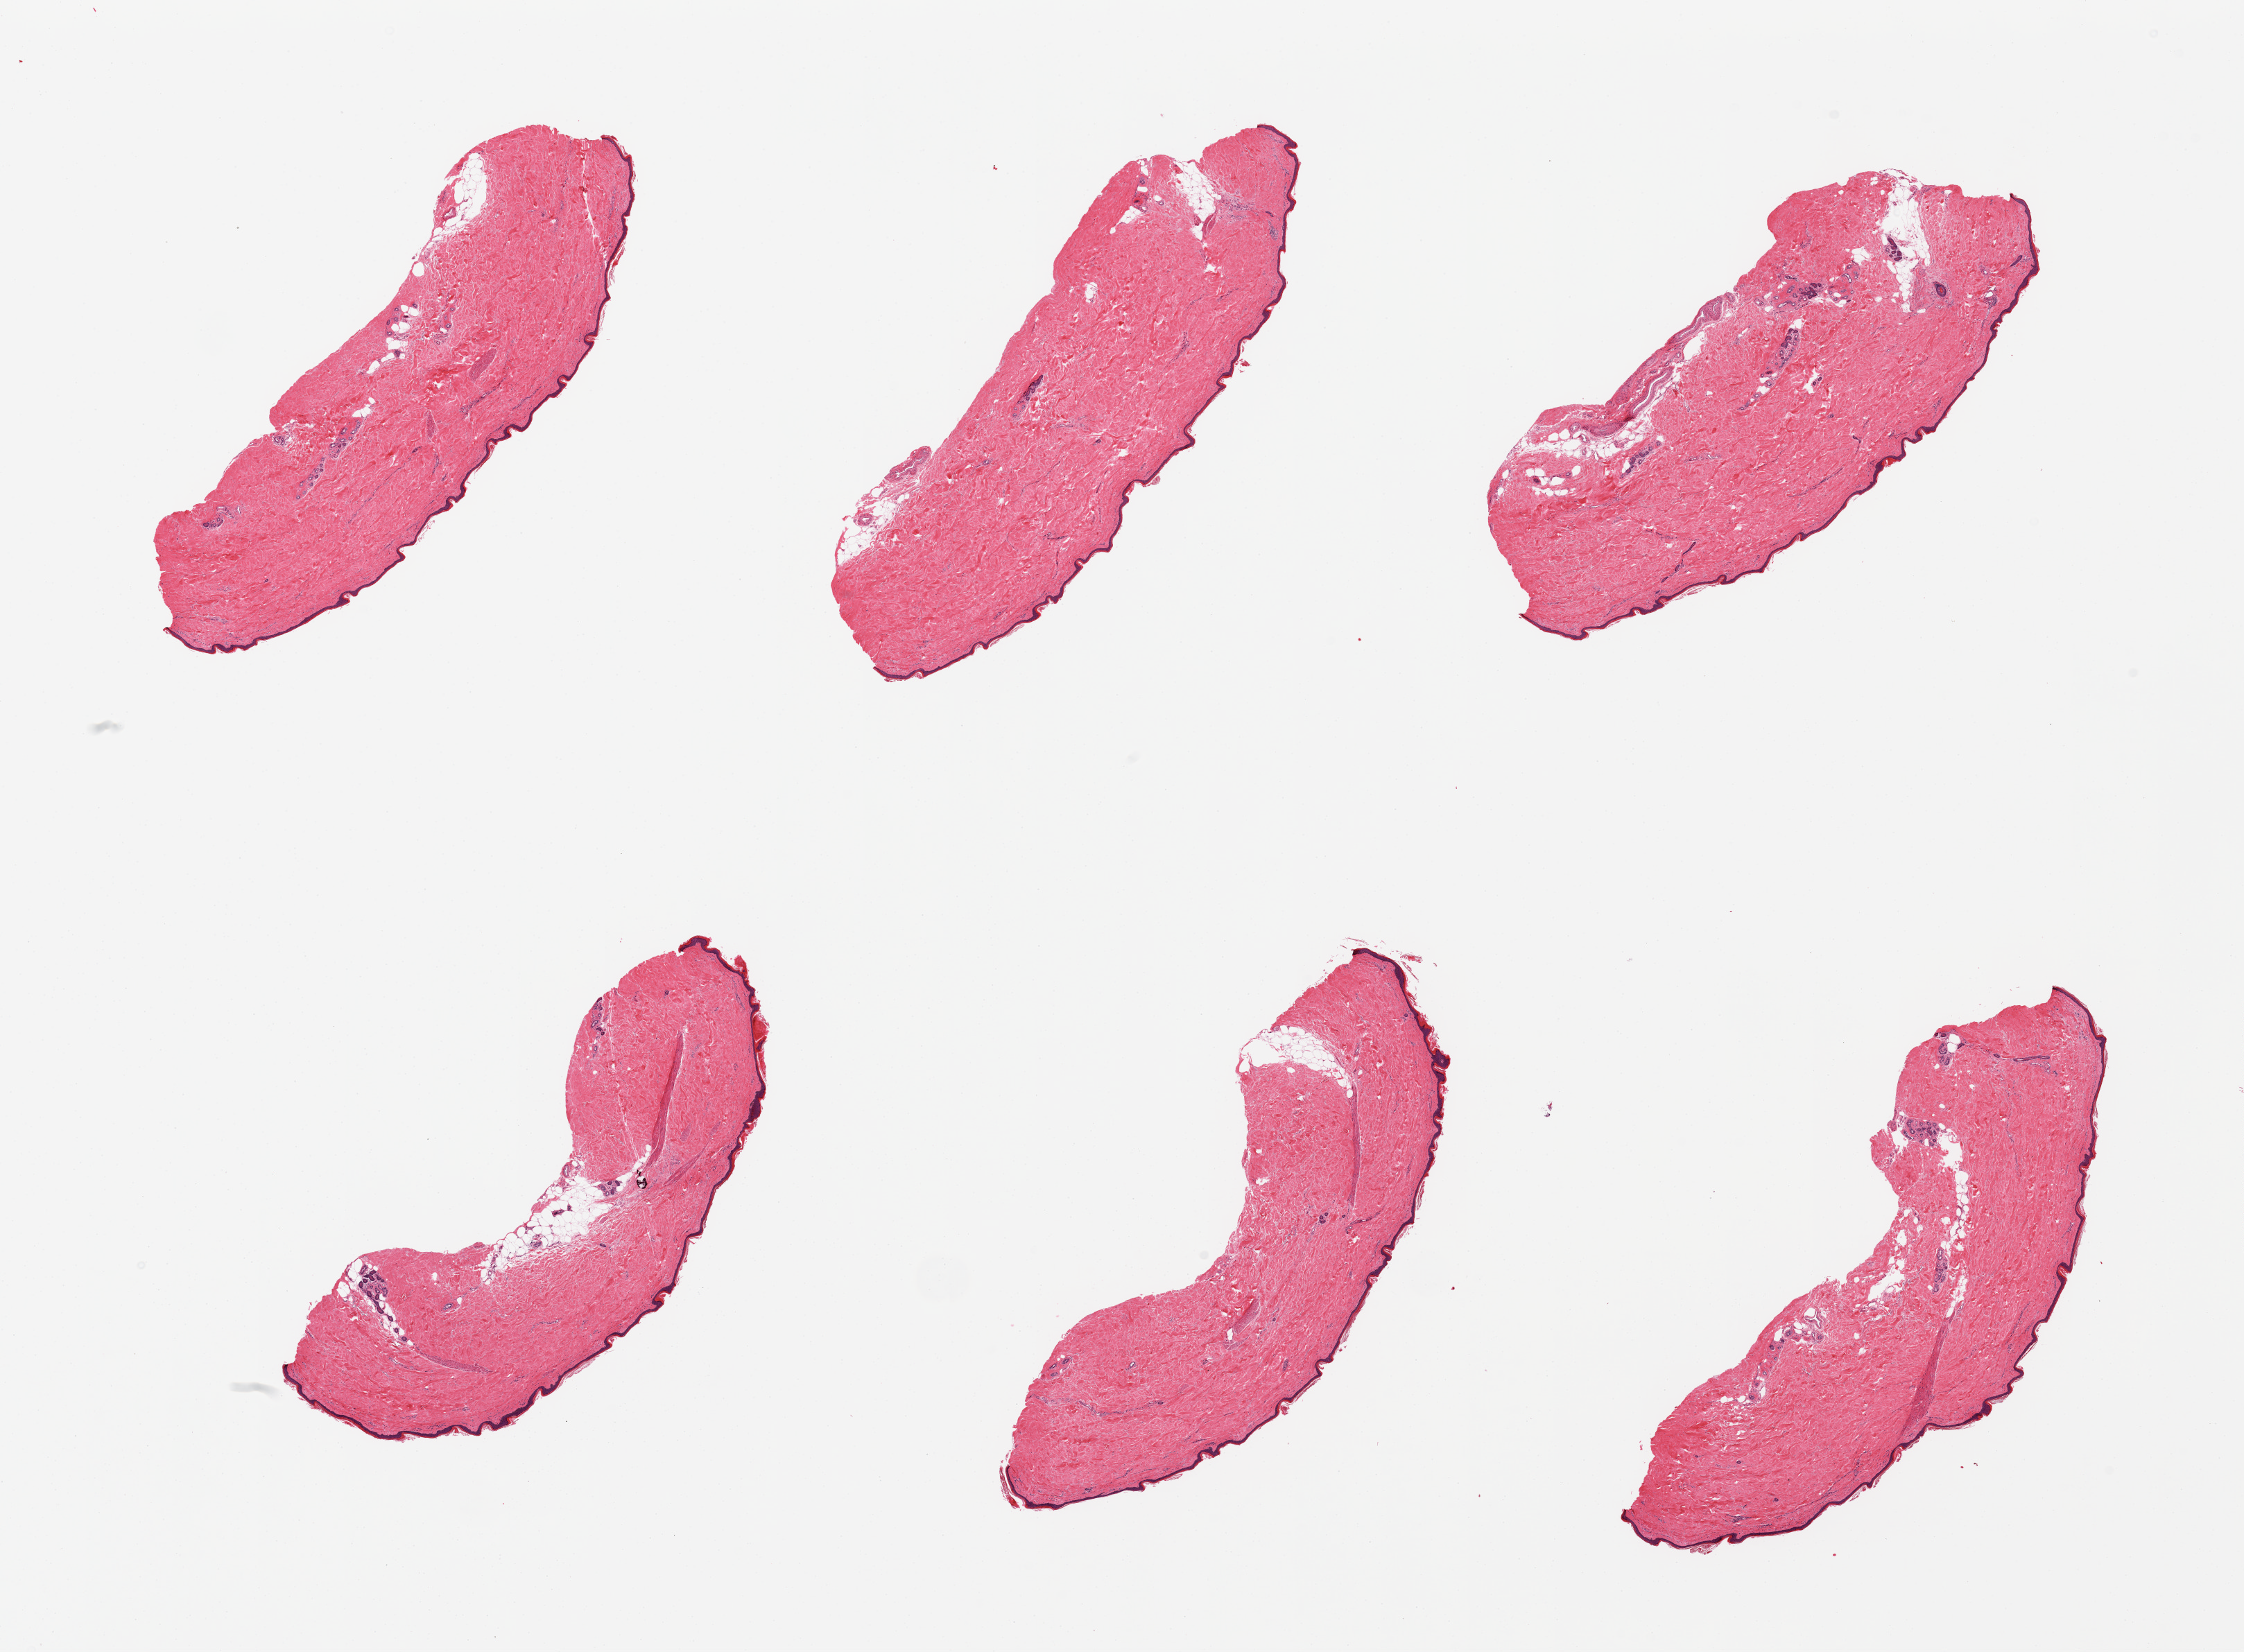
Whole-slide image, H&E stain — a low-resolution overview of the entire scanned area, about 25.6 x 18.8 mm (acquisition: 20x scan), PAXgene-fixed, paraffin-embedded tissue, sampled site (target tissue): skin of lower leg, tissue donor sample. Male donor.
- review note (as recorded): 6 pieces, fairly well trimmed, squamous epithelium measures 20-30 microns thick